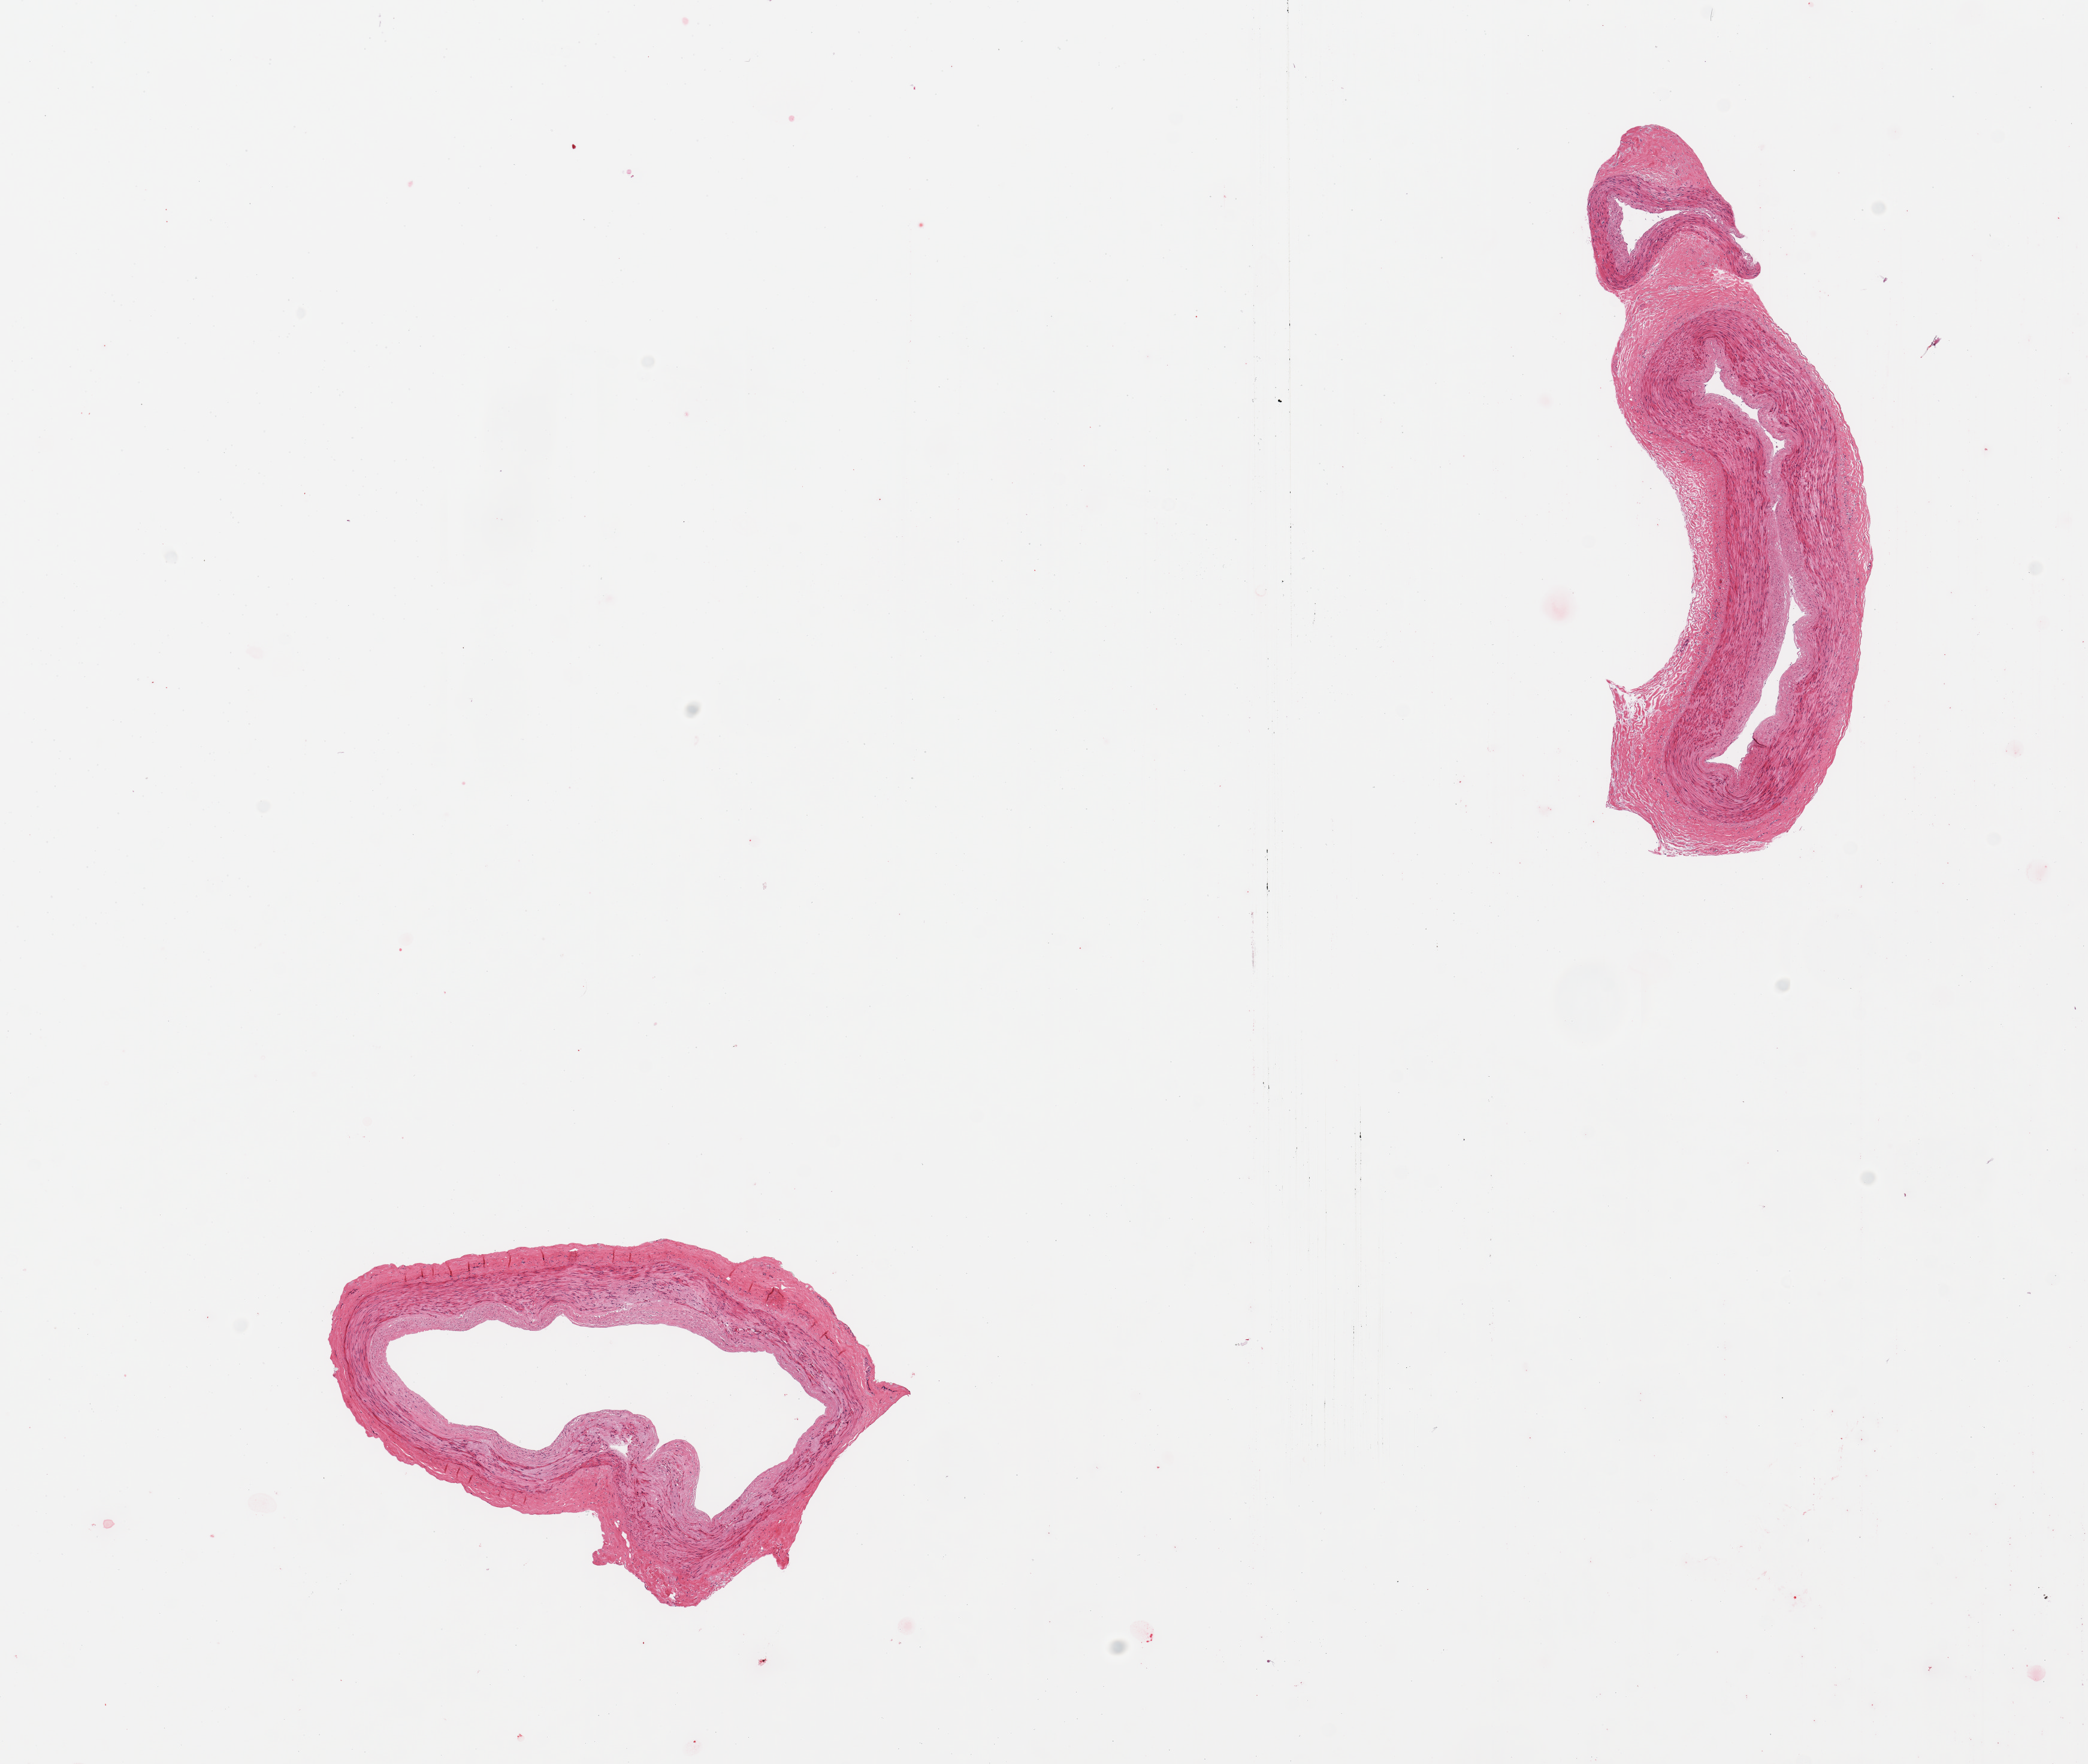
Digitized hematoxylin and eosin (H&E)-stained section, whole scanned area (about 13.8 x 11.6 mm, from a 20x scan) shown as a low-resolution overview. PAXgene-fixed paraffin-embedded (PFPE) section. Sampled site (target tissue): tibial artery. Tissue donor sample. Donor: male.
• review note (as recorded): 2 pieces; mild fibrous intimal thickening; well trimmed